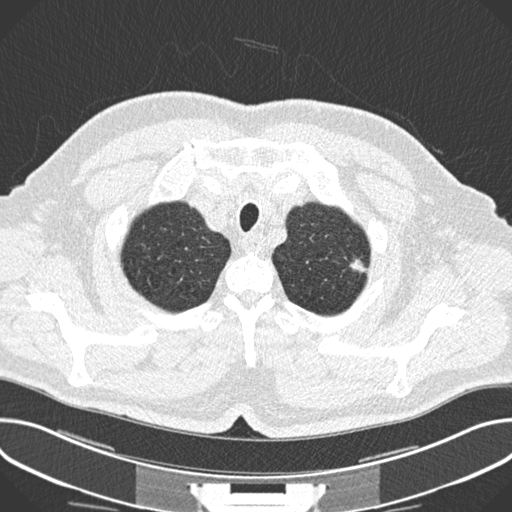
Chest CT (low-dose screening protocol), one axial image. Baseline annual screen. Lung window (W 1500 / L -600 HU). Male, age 63 years at enrolment. Current smoker at enrolment.
Expert-annotated lung lesion, box from (x=341, y=250) to (x=380, y=282) px. The screening reader recorded 2 non-calcified nodules or masses ≥4 mm on this exam (left upper lobe, left upper lobe); which of them this box marks is not recorded. Lung cancer was diagnosed 174 days after this screen: adenocarcinoma, NOS, left upper lobe, poorly differentiated (G3), stage IIIA (AJCC 6th edition), 11 mm at pathology.